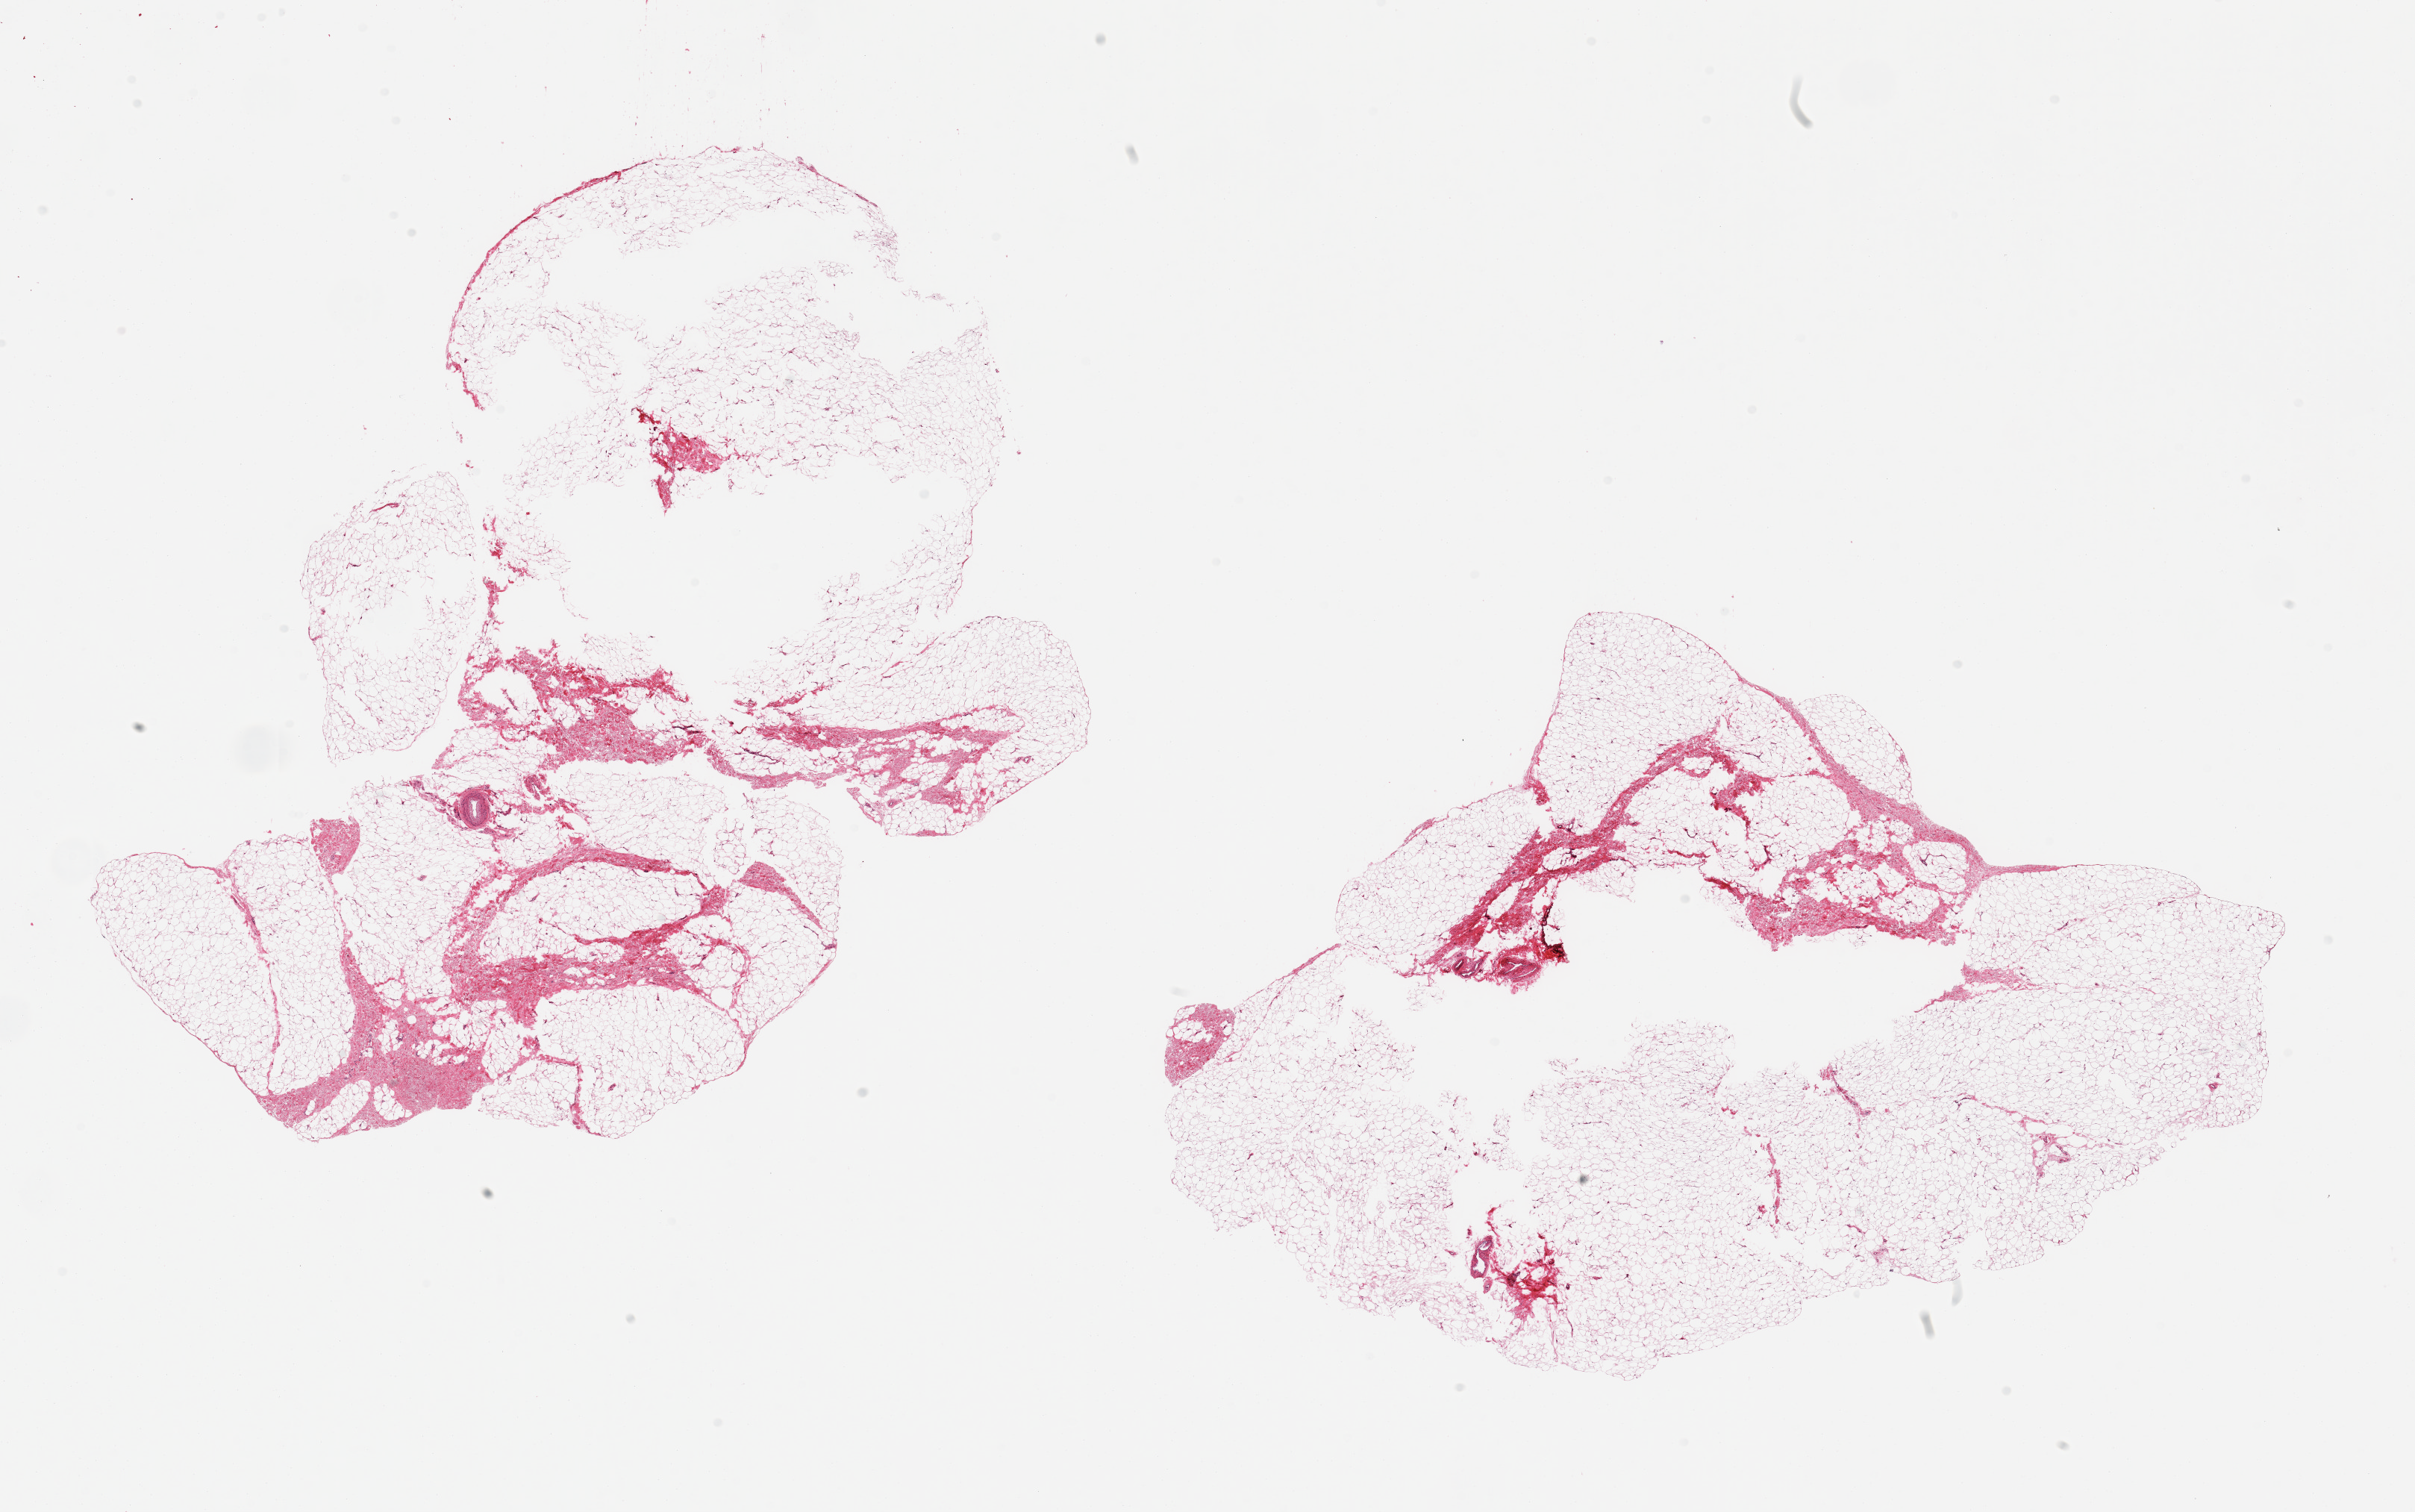
Haematoxylin and eosin whole-slide image, brightfield, low-resolution overview of the scanned area, about 25.6 x 16.0 mm (acquisition: 20x scan). PAXgene-fixed, paraffin-embedded tissue. Sampled site (target tissue): uterus. Donor tissue sample. Donor: female.
Reviewer comment on this tissue sample: 2 pieces; adipose tissue, no uterus.